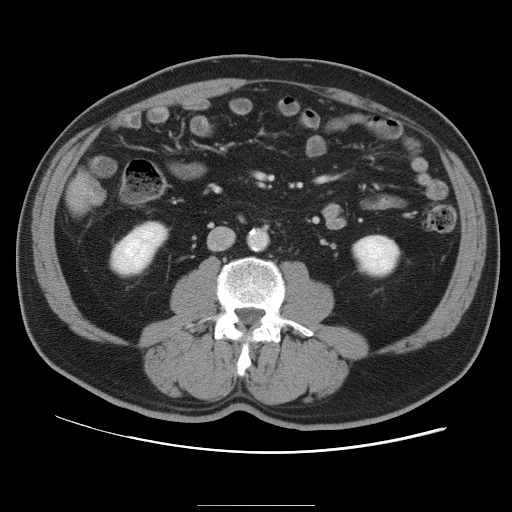
Contrast-enhanced abdominal CT, one axial slice. Slice 20 of 105 in the series (ordered by position). Intravenous contrast given. Soft-tissue window (W 400 / L 40 HU). 5 mm slice thickness. 512 × 512 image matrix. Male patient, age 64 years. From the clinical record (not read from this slice): diagnosis: colorectal cancer liver metastases, imaged before liver resection; multiple liver metastases: yes; largest metastasis: 3 cm.
Structures marked on this image (expert manual segmentation):
- liver: bounding box <69,180,90,209> (left, top, right, bottom; pixels)
- planned liver remnant (the part of the liver to remain after resection): <68,181,90,209>